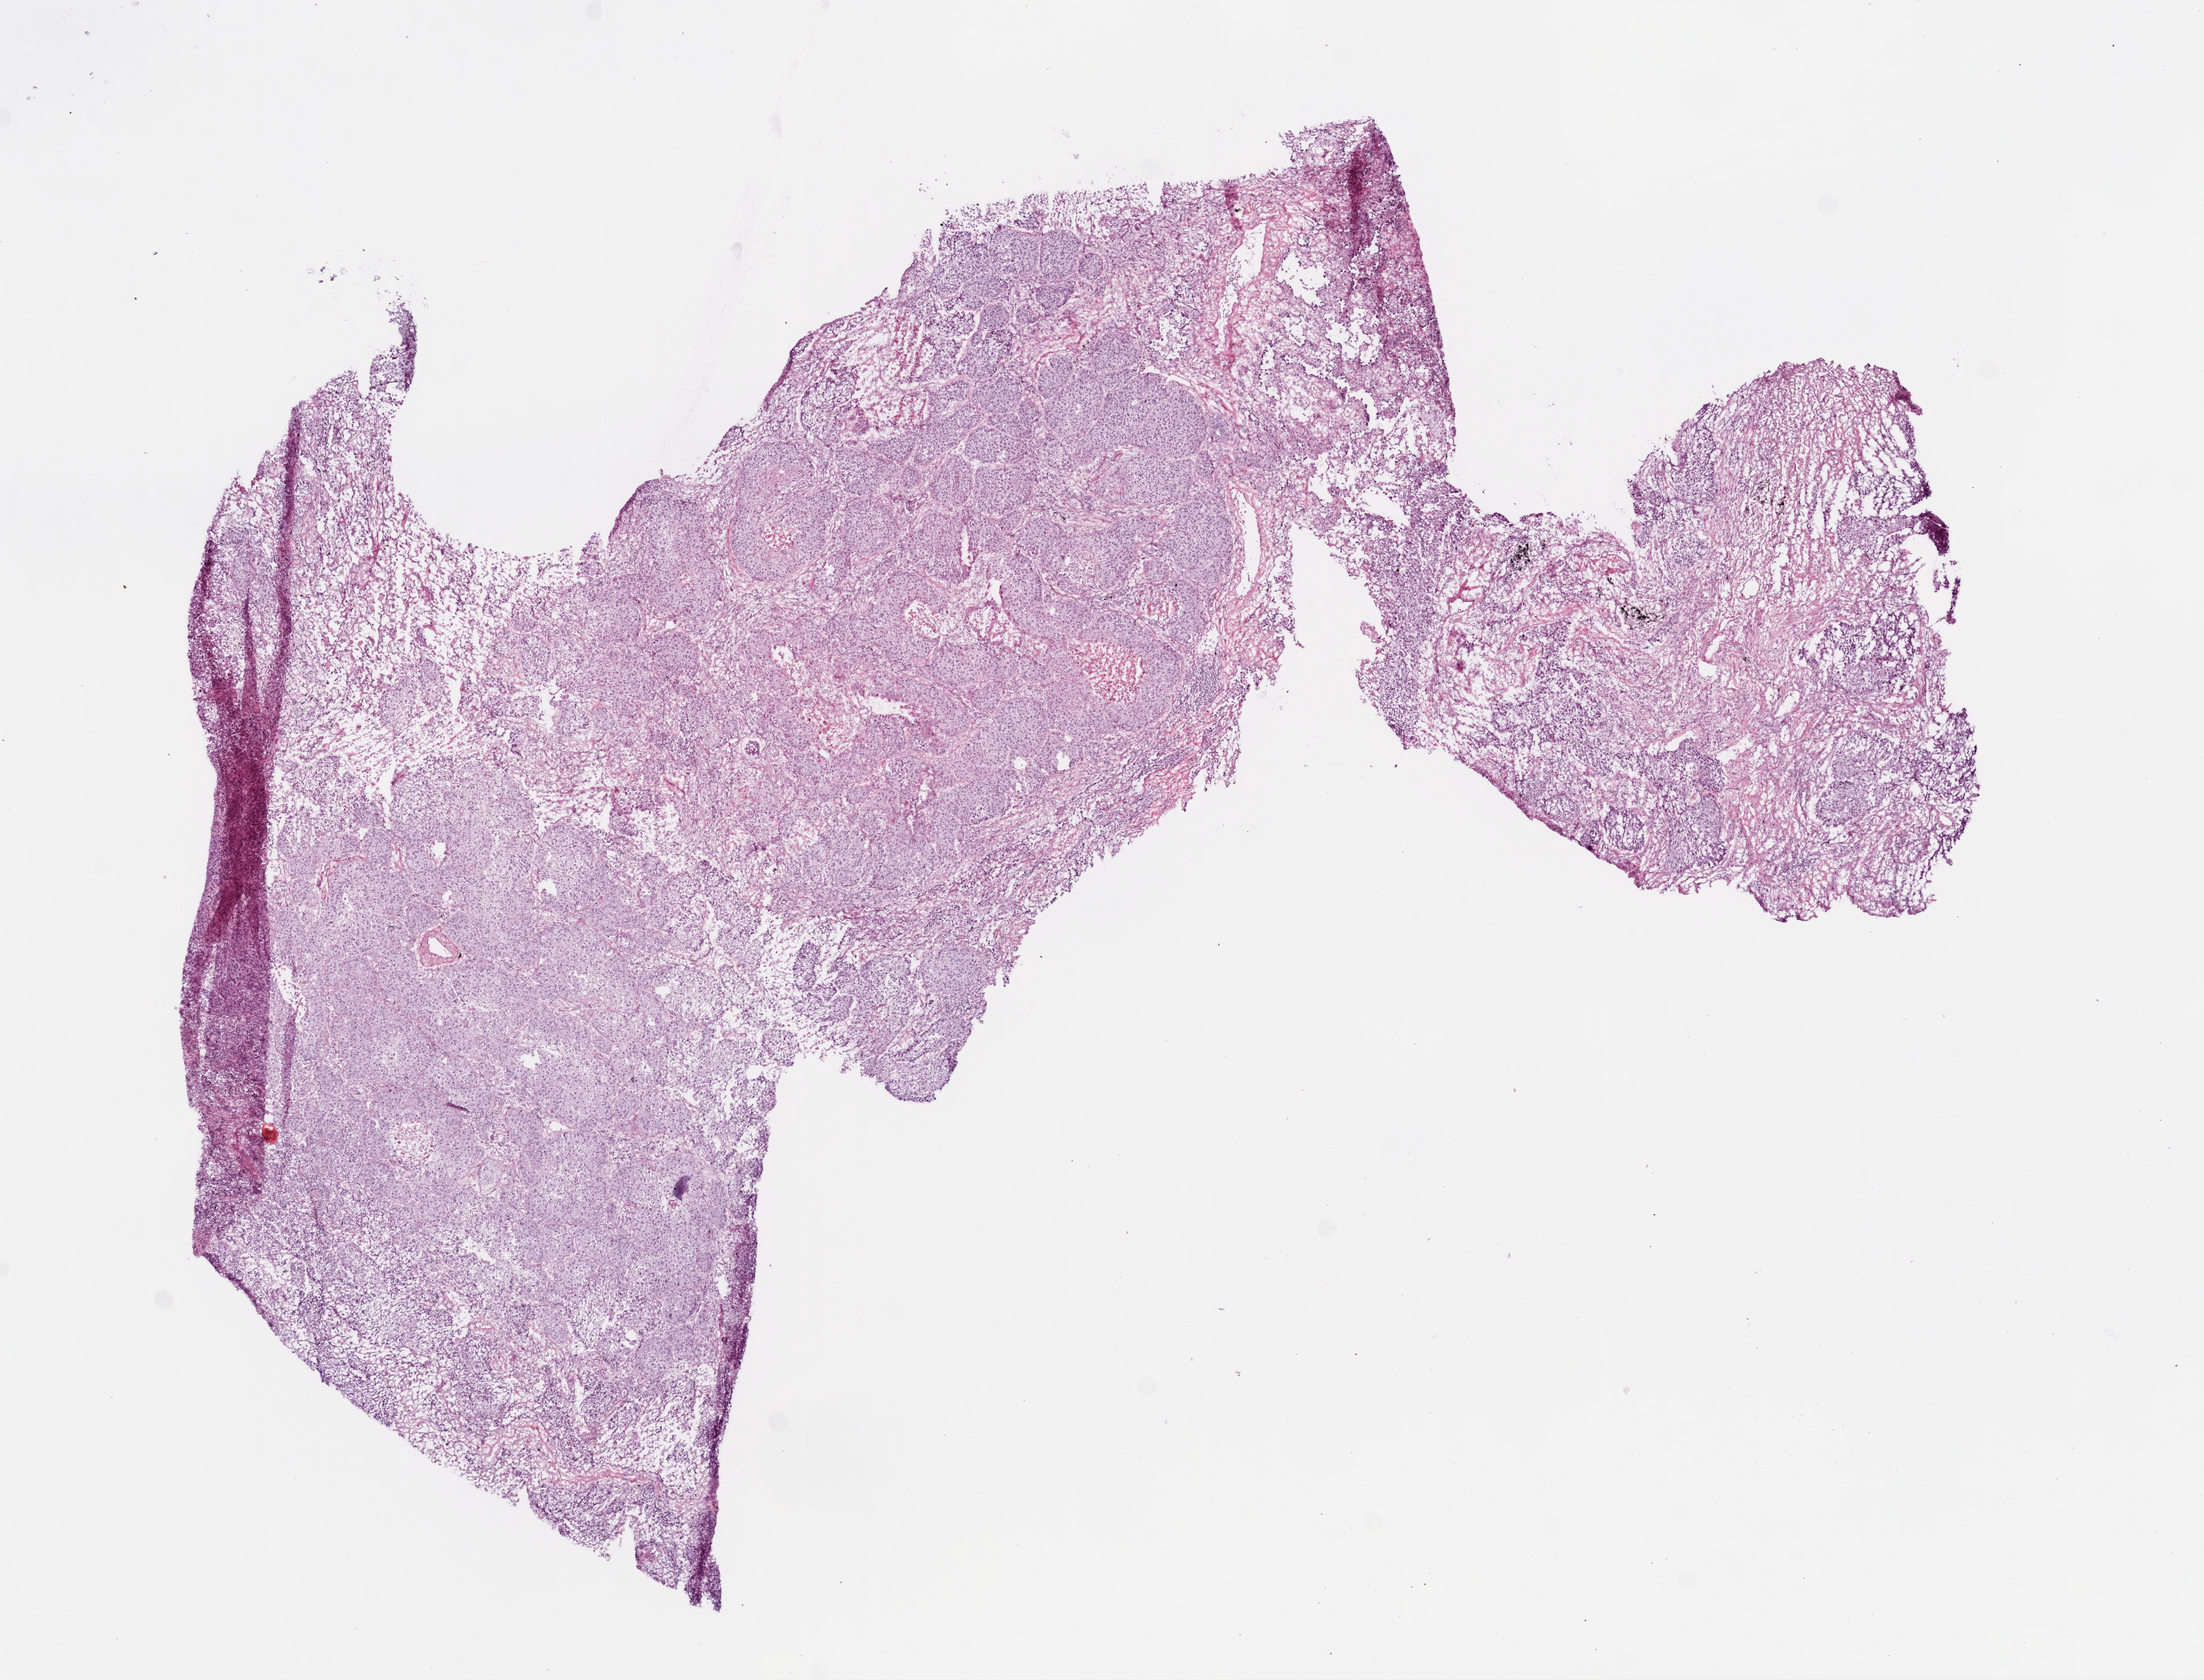
Digitized Hematoxylin and eosin (H&E) stained tissue section (whole slide) — whole scanned area (about 11.0 x 8.4 mm, acquisition: 20x scan) shown as a low-resolution overview, frozen section from the top of the tissue portion, sample: primary tumour, lung. Male patient. Slide review estimates, as recorded: tumour cells 83%, tumour nuclei 75%.
Histologic diagnosis: Squamous cell carcinoma, NOS.